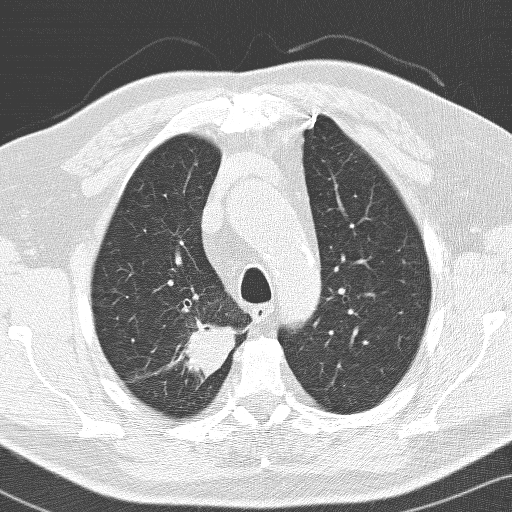
Chest CT (low-dose screening protocol), one axial image. Baseline screening round. Lung window (W 1500 / L -600 HU). 120 kVp. Slice 31 of 141 in the series. Male participant, aged 66 years at enrolment. Former smoker at enrolment.
- Expert-annotated lung lesion, bounding box [x1, y1, x2, y2] px = [152, 309, 232, 393].
- The exam's reader record, not a measurement of the box and not confirmed to be the same lesion: non-calcified nodule or mass ≥4 mm, right upper lobe, 36 × 30 mm, spiculated (stellate) margins, soft tissue attenuation.
- Official screen result: positive, change unspecified: nodule(s) >= 4 mm or enlarging nodule(s), mass(es), or other non-specific abnormalities suspicious for lung cancer.
- Lung cancer was diagnosed 103 days after this screen: adenocarcinoma, NOS, right upper lobe, poorly differentiated (G3), stage IIB (AJCC 6th edition), 33 mm at pathology.